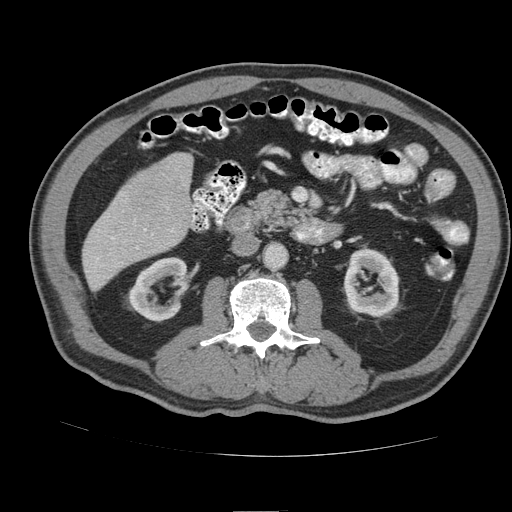
Contrast-enhanced abdominal CT (liver protocol), one axial slice; position 28 of 105 along the scan axis; 140 kVp; soft-tissue window (W 400 / L 40 HU); 2.5 mm slice thickness; 512 × 512 image matrix, field of view 380 × 380 mm. From the clinical record (not read from this slice): diagnosis: hepatocellular carcinoma (patient treated with transarterial chemoembolisation; whether this scan precedes or follows treatment is not stated here); TNM stage (as recorded): Stage-IIIB; Child-Pugh class: A.
Annotated regions visible in this slice (semi-automatic segmentation, software-assisted and operator-edited):
- liver parenchyma outside the tumour (the mass and vessels are separate outlines, so this box may not span the whole liver): box from (x=84, y=259) to (x=90, y=270) px
- mass: (x=126, y=167)–(x=185, y=219)